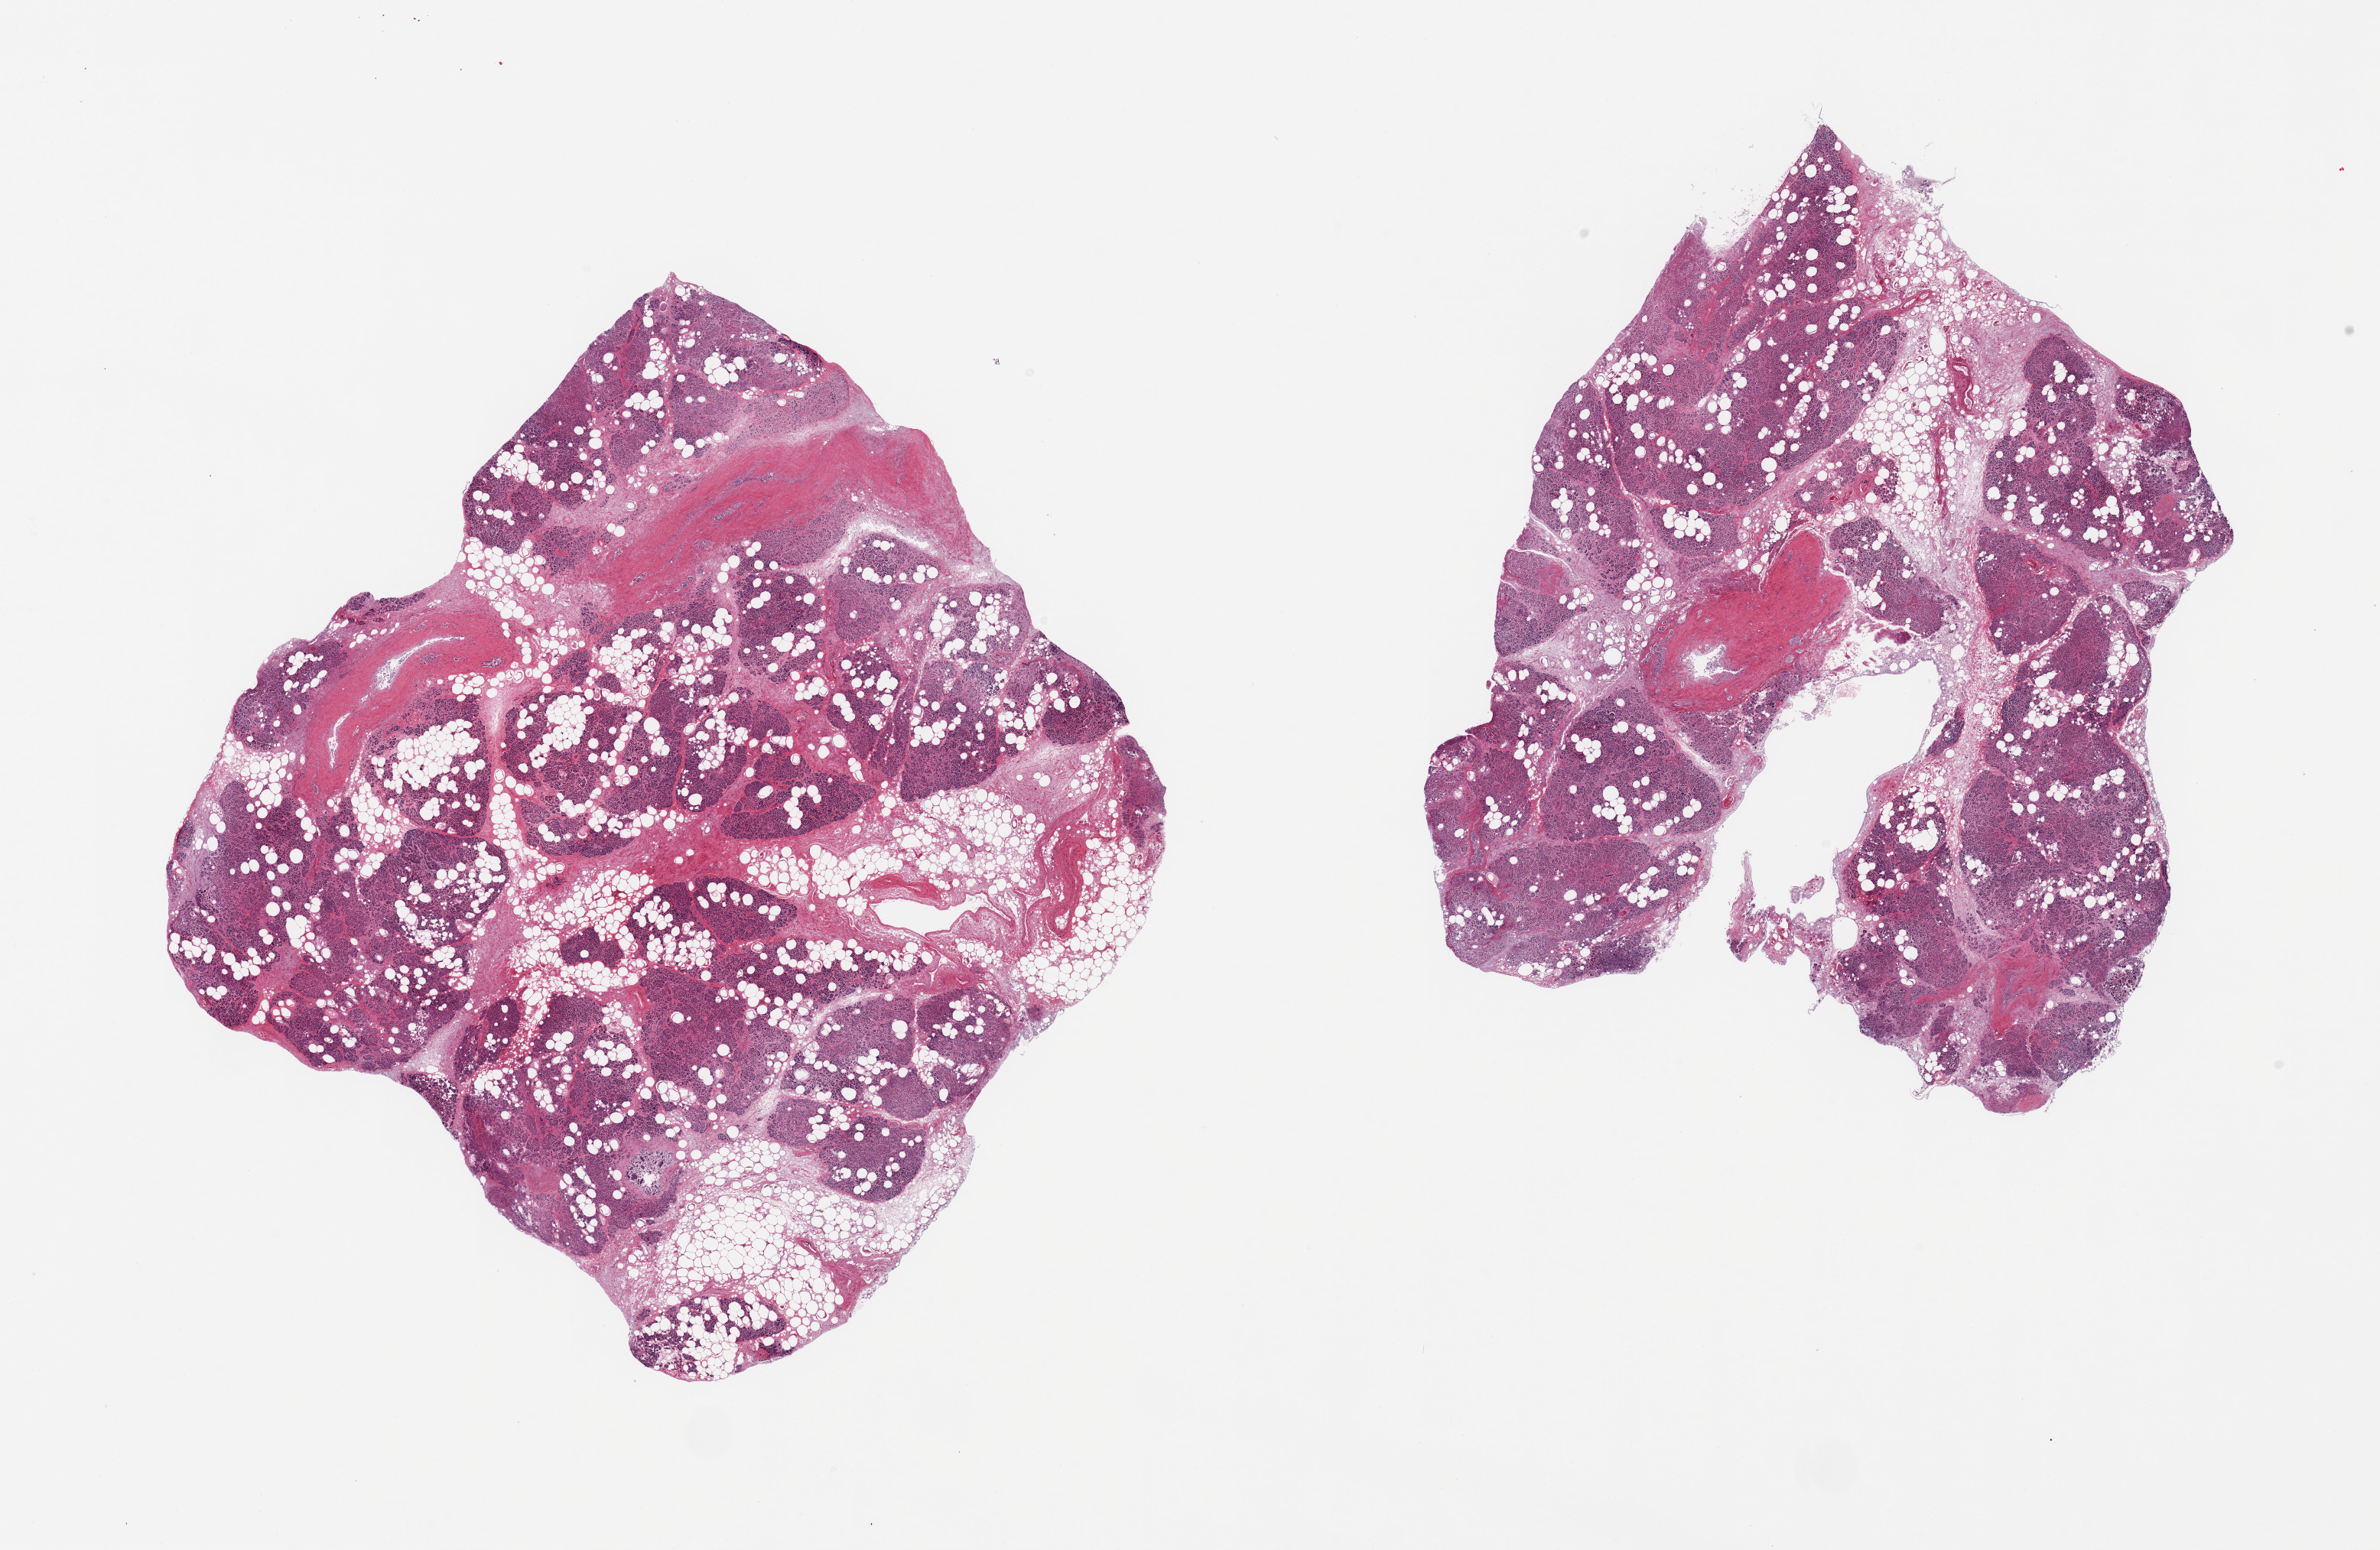
Whole-slide image, haematoxylin and eosin stain, brightfield, low-resolution overview of the scanned area, about 24.6 x 16.0 mm (slide scanned at 20x); PAXgene-fixed, paraffin-embedded tissue; sampled site (target tissue): pancreas; donor tissue sample.
Reviewer comment on this tissue sample: 2 pieces; 50% internal fat content.